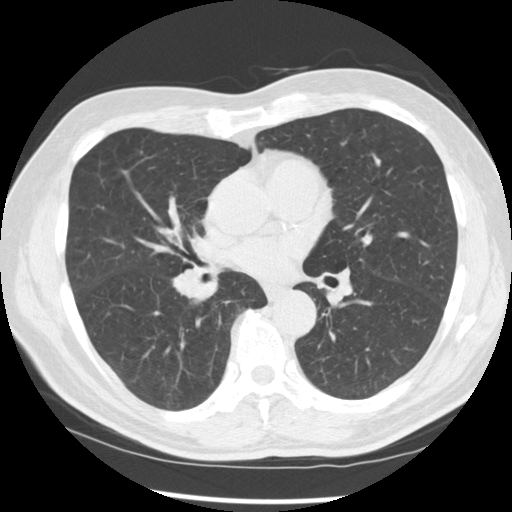
Low-dose screening chest CT, one axial slice; slice 144 of 277 in the series (ordered by position); 120 kVp; lung window (W 1500 / L -600 HU); 2.5 mm slice thickness; 512 × 512 image matrix, field of view 365 × 365 mm.
Annotated regions visible in this slice (manually delineated by an expert):
- lesion 1 (tumor, middle lobe of right lung): box from (x=172, y=267) to (x=208, y=304) px